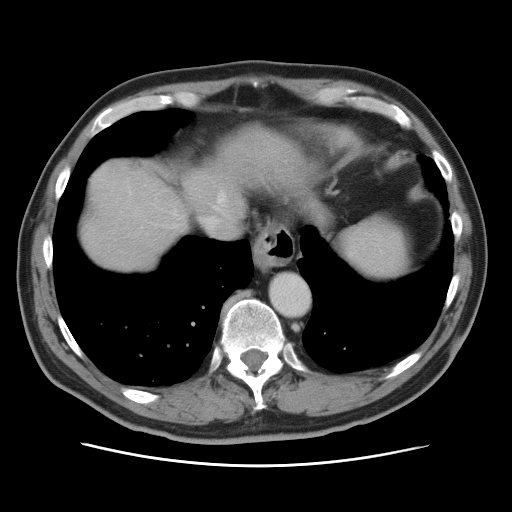
Contrast-enhanced abdominal CT, one axial slice. Position 70 of 80 along the scan axis. Soft-tissue window (W 400 / L 40 HU). 5 mm slice thickness. 512 × 512 image matrix, field of view 370 × 370 mm. Male patient, age 69 years. Case-level facts recorded for this patient, not image findings: diagnosis: colorectal cancer liver metastases, imaged before liver resection; multiple liver metastases: no; largest metastasis: 5 cm; disease in both lobes: yes.
Outlined on this slice (manually delineated by an expert):
- hepatic veins: bounding box (x1, y1, x2, y2) in pixels: (120, 181, 226, 231)
- liver: (79, 133, 293, 270)
- planned liver remnant (the part of the liver to remain after resection): (79, 142, 254, 269)